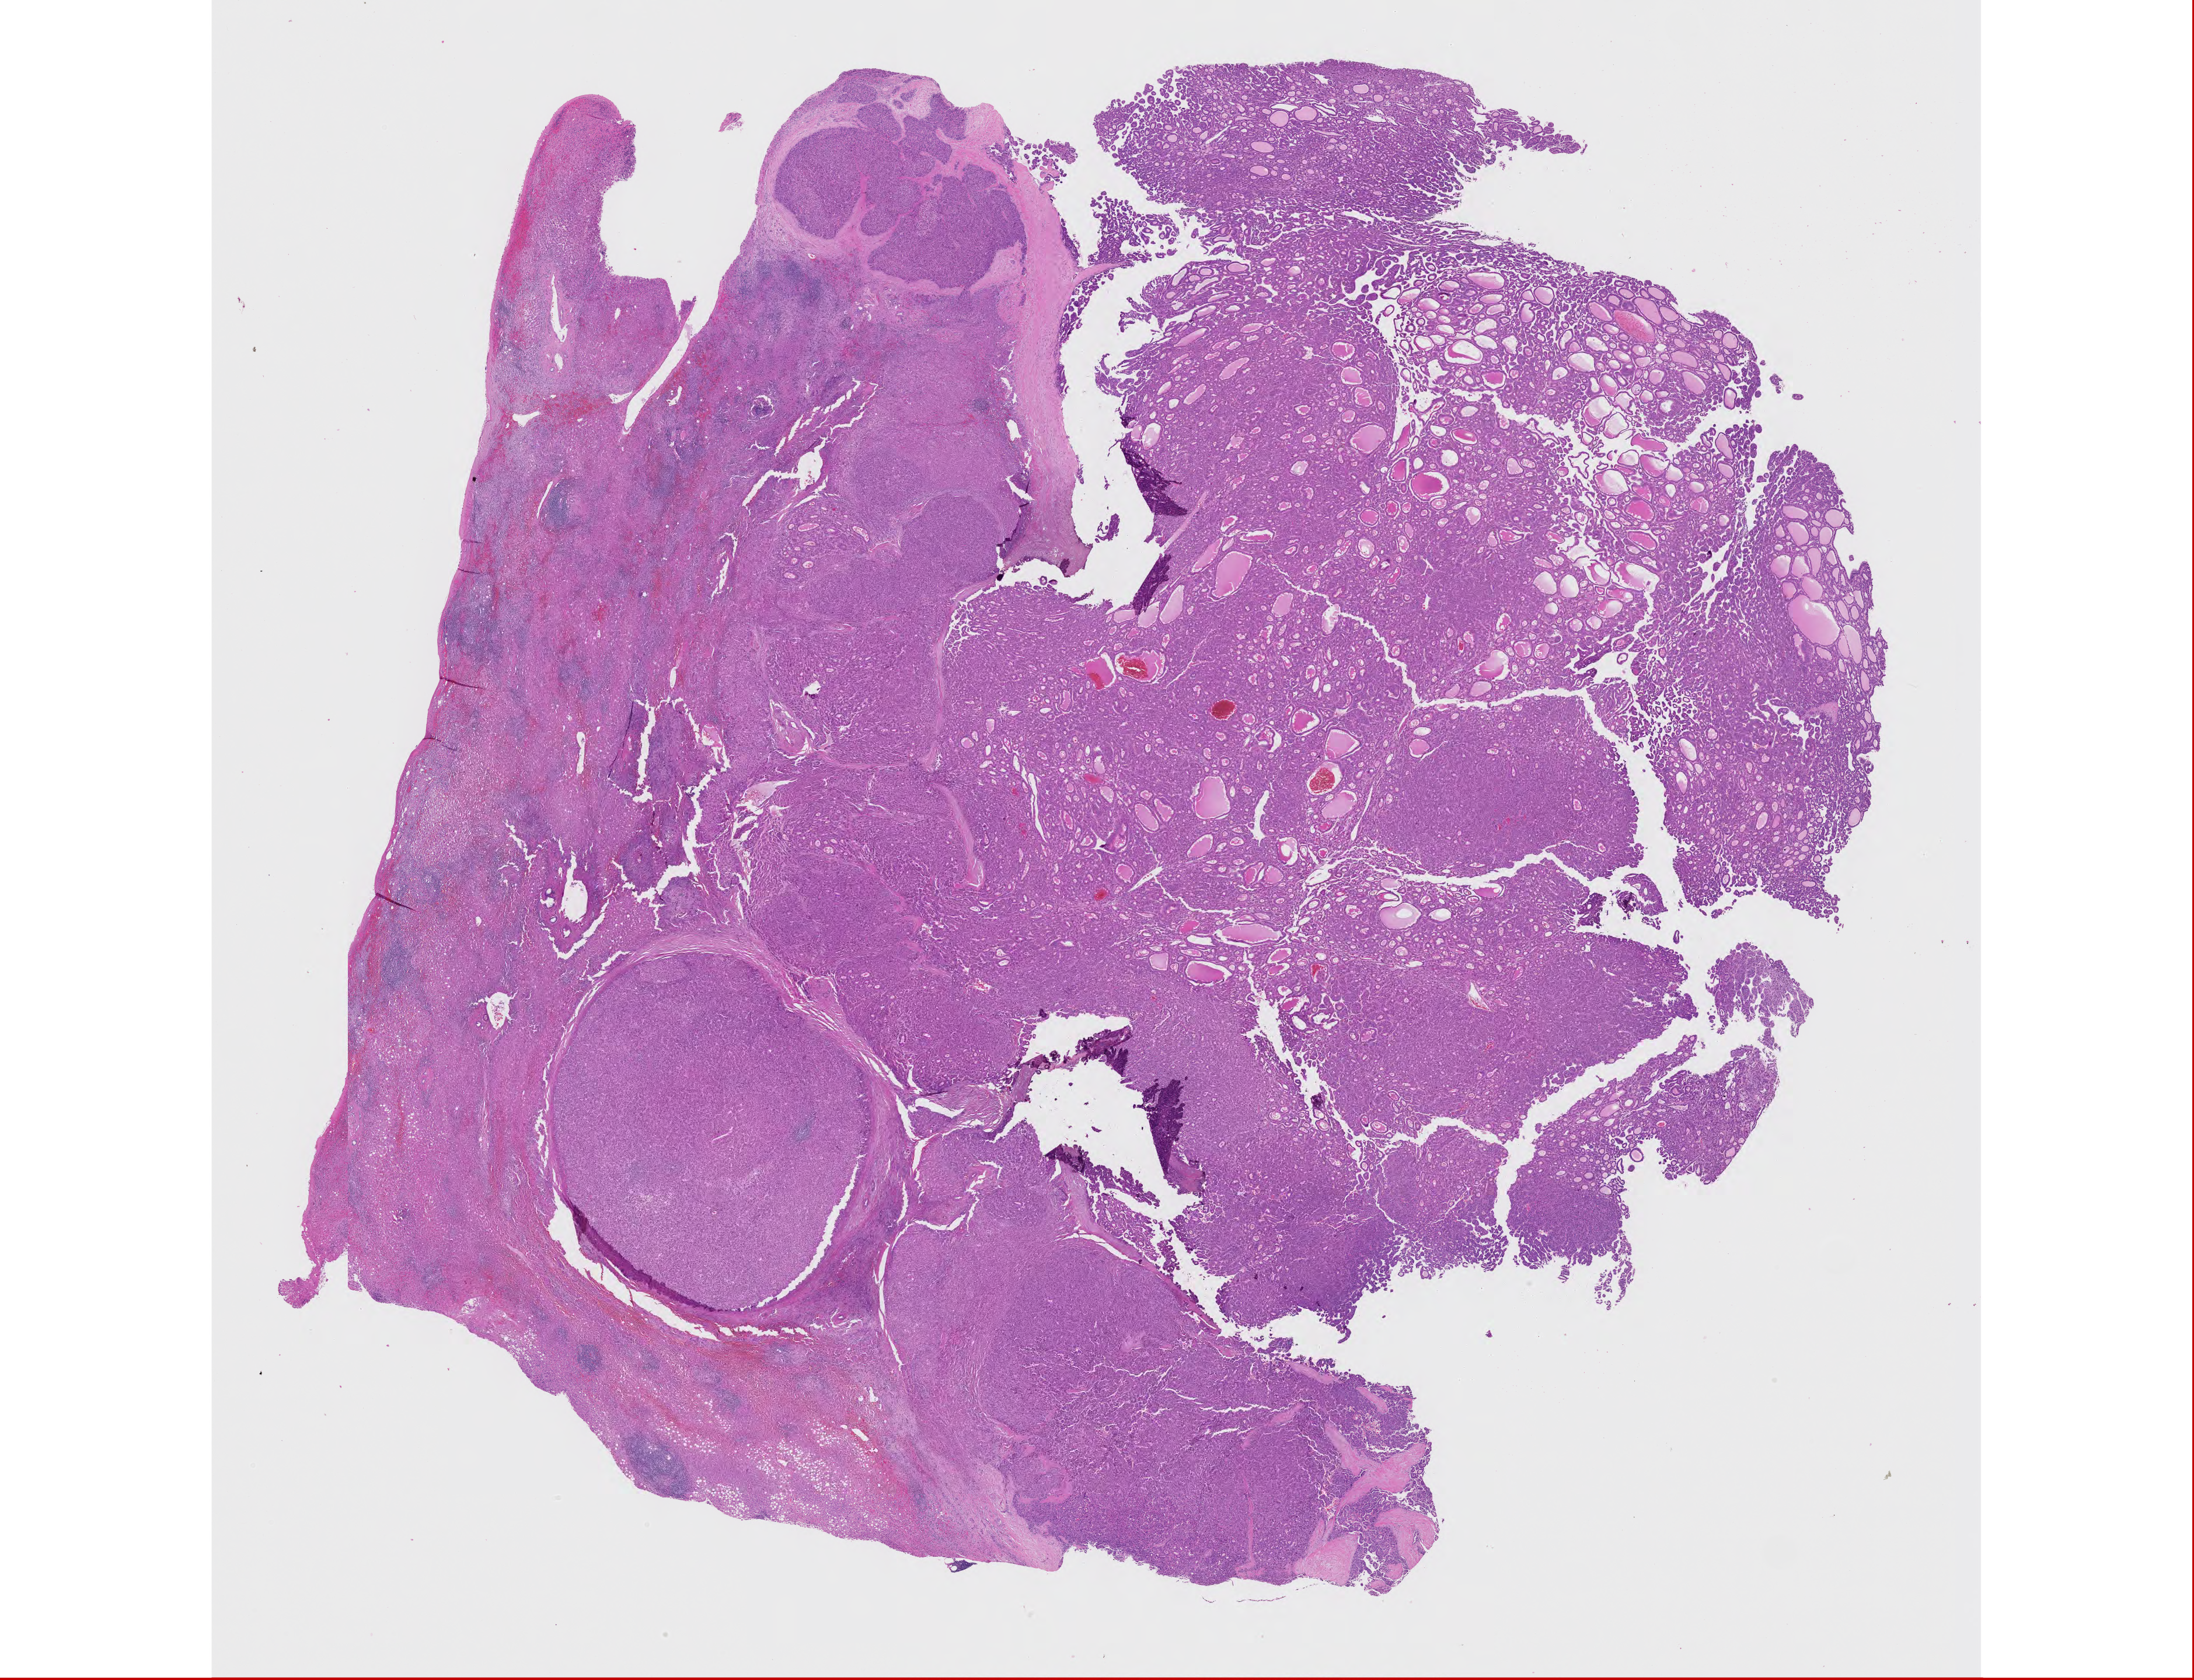
H&E whole-slide image — a low-resolution overview of the entire scanned area, about 30.1 x 23.0 mm (from a 20x scan). FFPE section. Liver, primary tumour sample. Patient: male, age at initial diagnosis 66 years. Histologic grade: G1 (well differentiated).
• AJCC pathologic stage: I (7th edition)
• diagnosis: Hepatocellular carcinoma, NOS